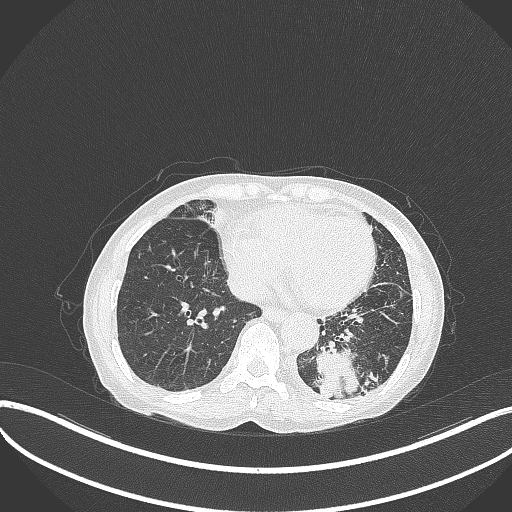
Chest CT, one axial slice; position 92 of 370 along the scan axis; reconstruction kernel B70f; lung window (W 1500 / L -600 HU); 512 × 512 image matrix, field of view 400 × 400 mm. Patient: female, 78 years. Case-level facts recorded for this patient, not image findings: clinical TNM (as recorded): T3 N0 M1.
Outlined on this slice (bounding box drawn by a radiologist):
- lung tumour (recorded histology: squamous cell carcinoma): bounding box [x1, y1, x2, y2] px = [315, 341, 365, 402]